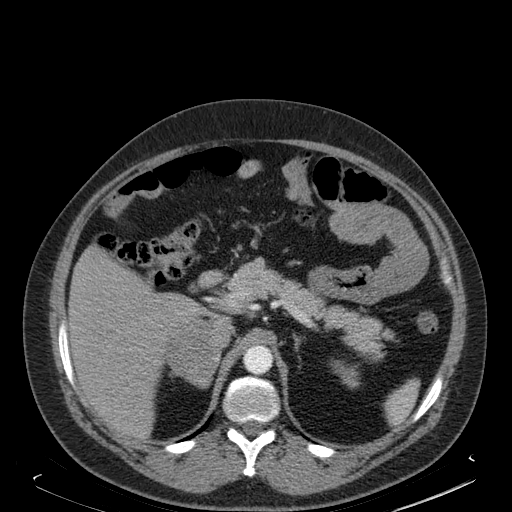
Contrast-enhanced abdominal CT, one axial slice; soft-tissue window (W 400 / L 40 HU); 1.5 mm slice thickness; 512 × 512 image matrix. Male patient. Case-level facts recorded for this patient, not image findings: diagnosis: adrenocortical carcinoma; tumour side: right adrenal; tumour size at pathology: 7.5 cm; Ki-67 index: 25 %; stage (as recorded): 4.
Annotated regions visible in this slice (semi-automatically segmented with operator editing):
- mass: box from (x=166, y=321) to (x=220, y=384) px